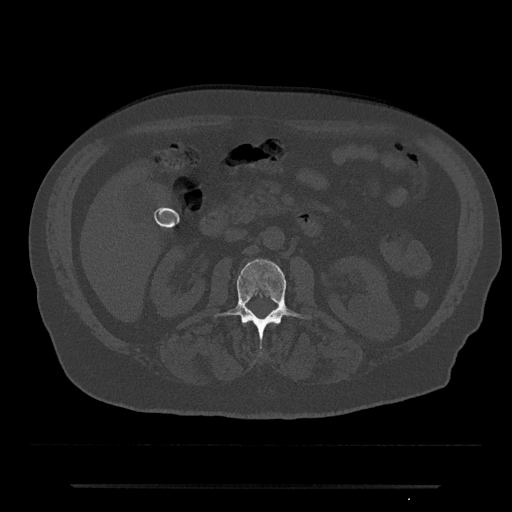
CT including the spine, one axial slice; position 473 of 797 along the scan axis; reconstruction kernel Br40s/3; 120 kVp; bone window (W 1800 / L 400 HU); 0.5 mm slice thickness; 512 × 512 image matrix. Male patient, age 80 years. Case-level facts recorded for this patient, not image findings: primary cancer: prostate; vertebrae with lytic lesions (as recorded): L1, T11.
Outlined on this slice (semi-automatic segmentation, software-assisted and operator-edited):
- L2 vertebra: box from (x=215, y=259) to (x=312, y=353) px